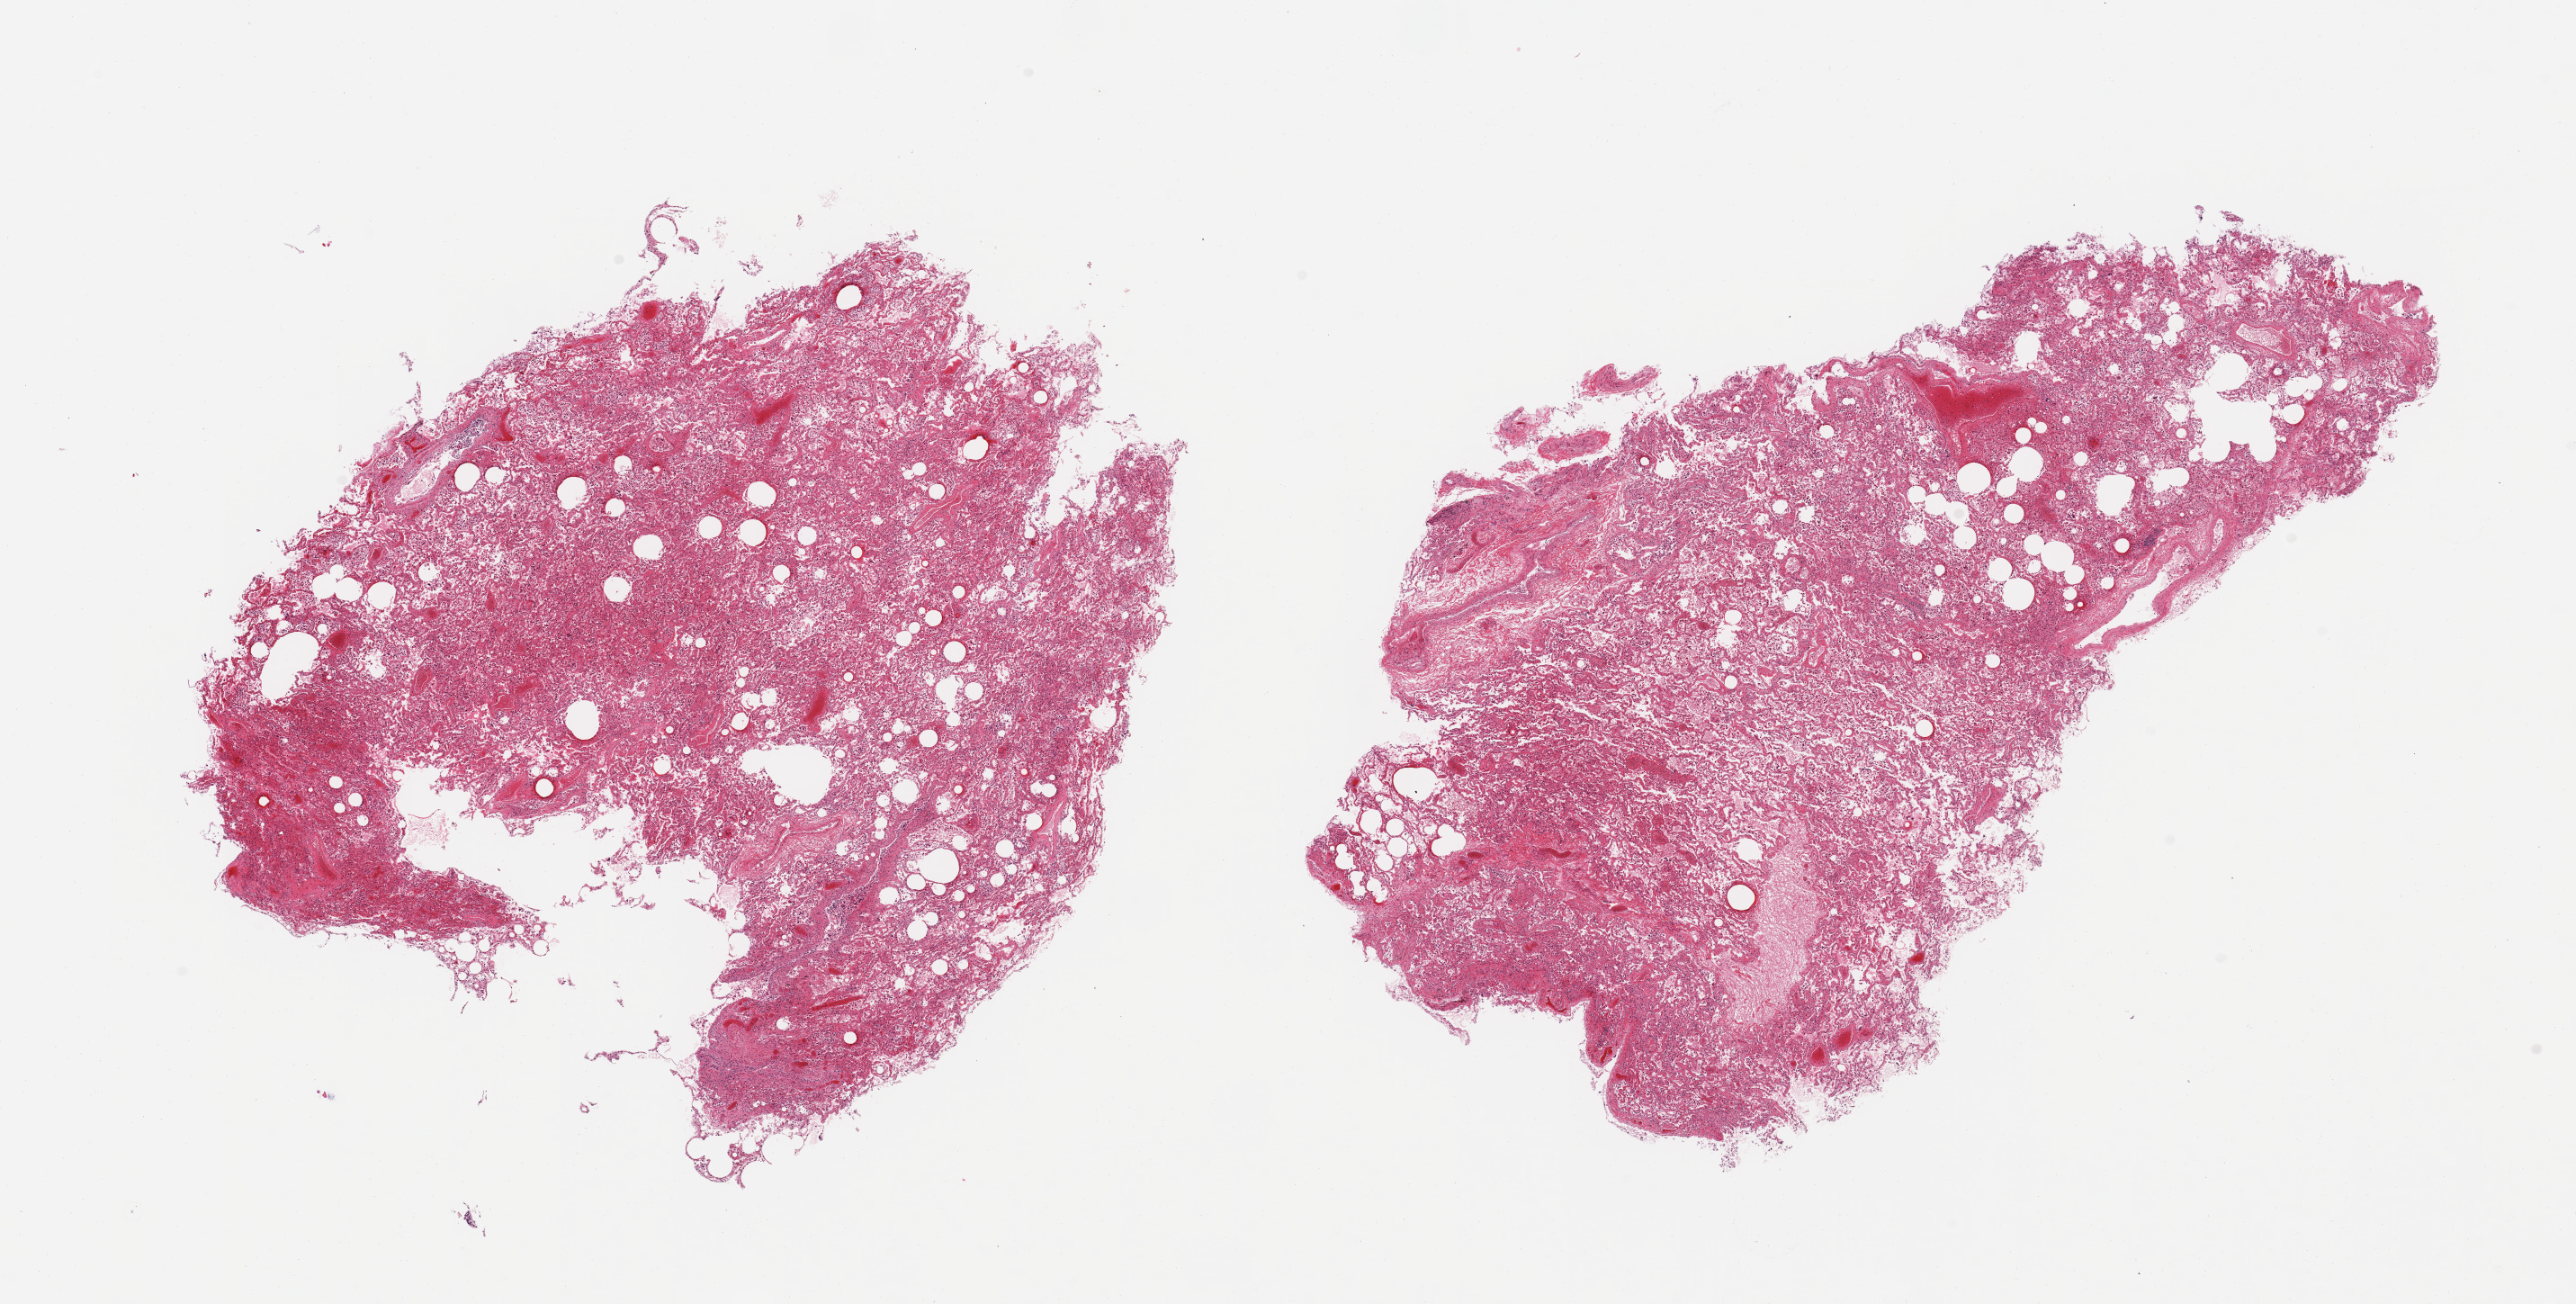
Hematoxylin and eosin (H&E) whole-slide image, brightfield — shown as a low-resolution overview of the whole scanned area (about 22.6 x 11.5 mm), PAXgene-fixed, paraffin-embedded tissue, target tissue: lung, tissue donor sample.
Pathologist's review note for this sample: 2 pieces; marked congestion.